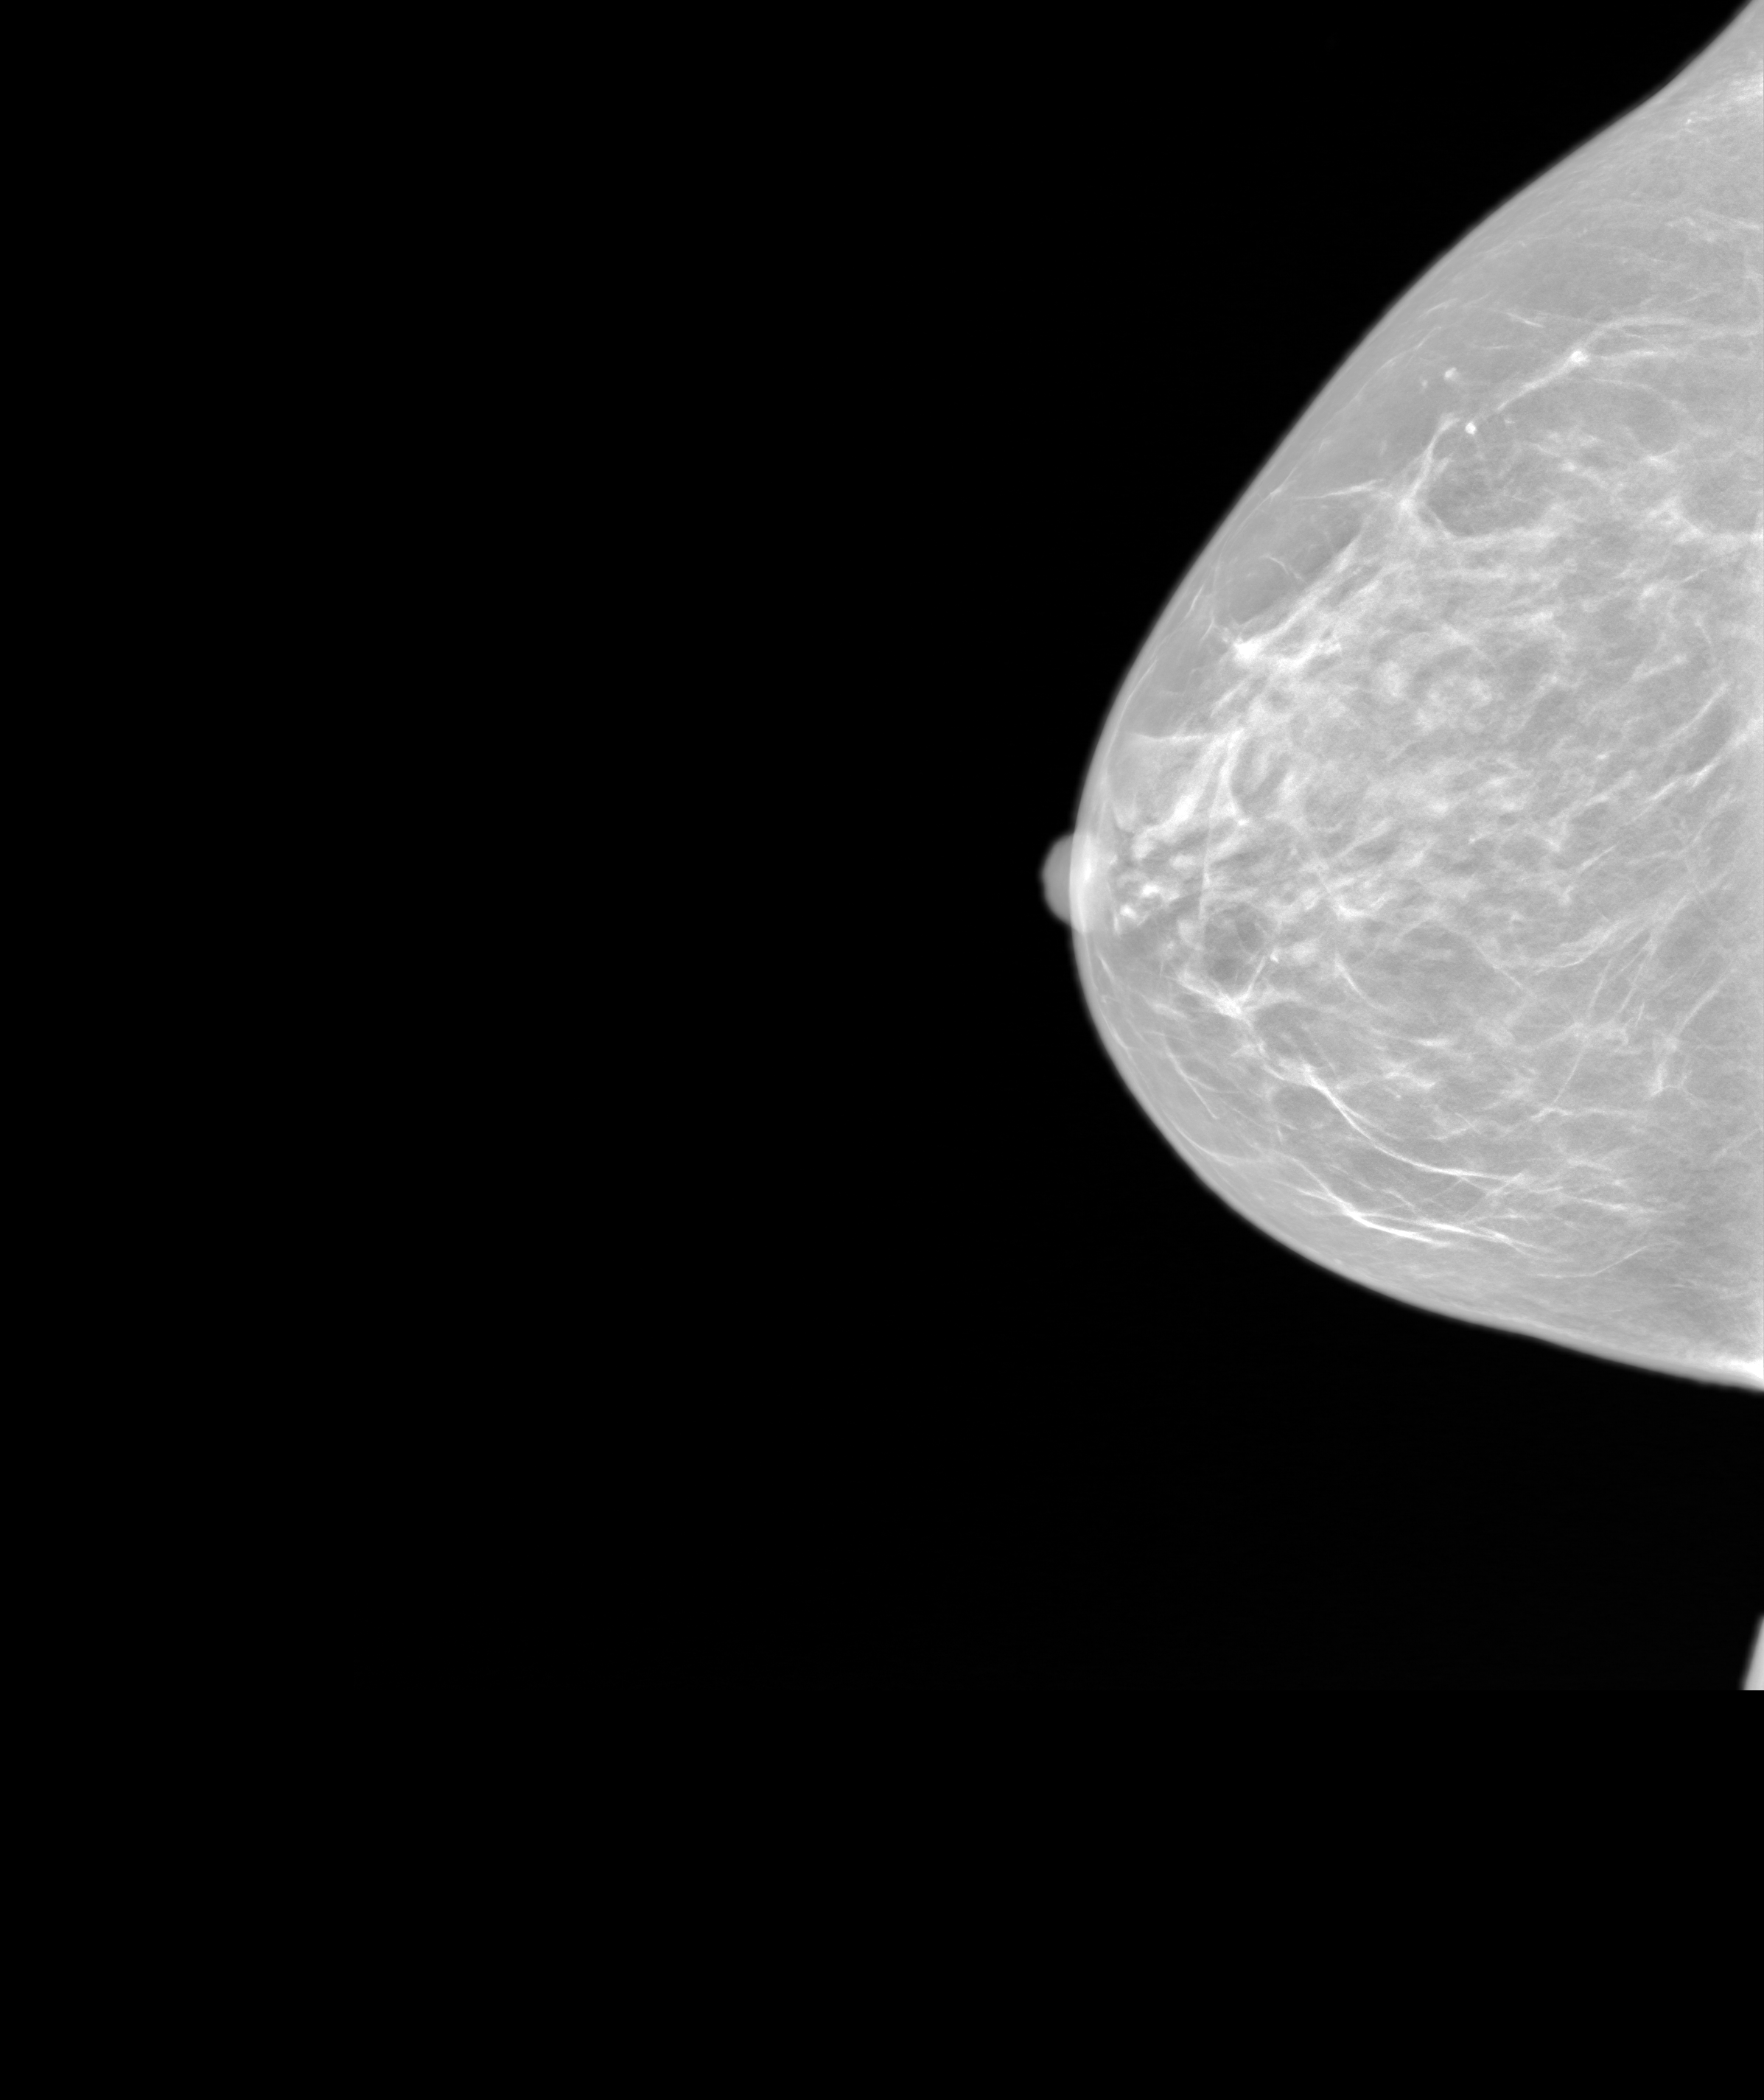
Annual screening mammography examination. Female patient, age 57 years.
Image type: synthesized 2-D view from tomosynthesis. Breast: right. Projection: craniocaudal (CC) view.